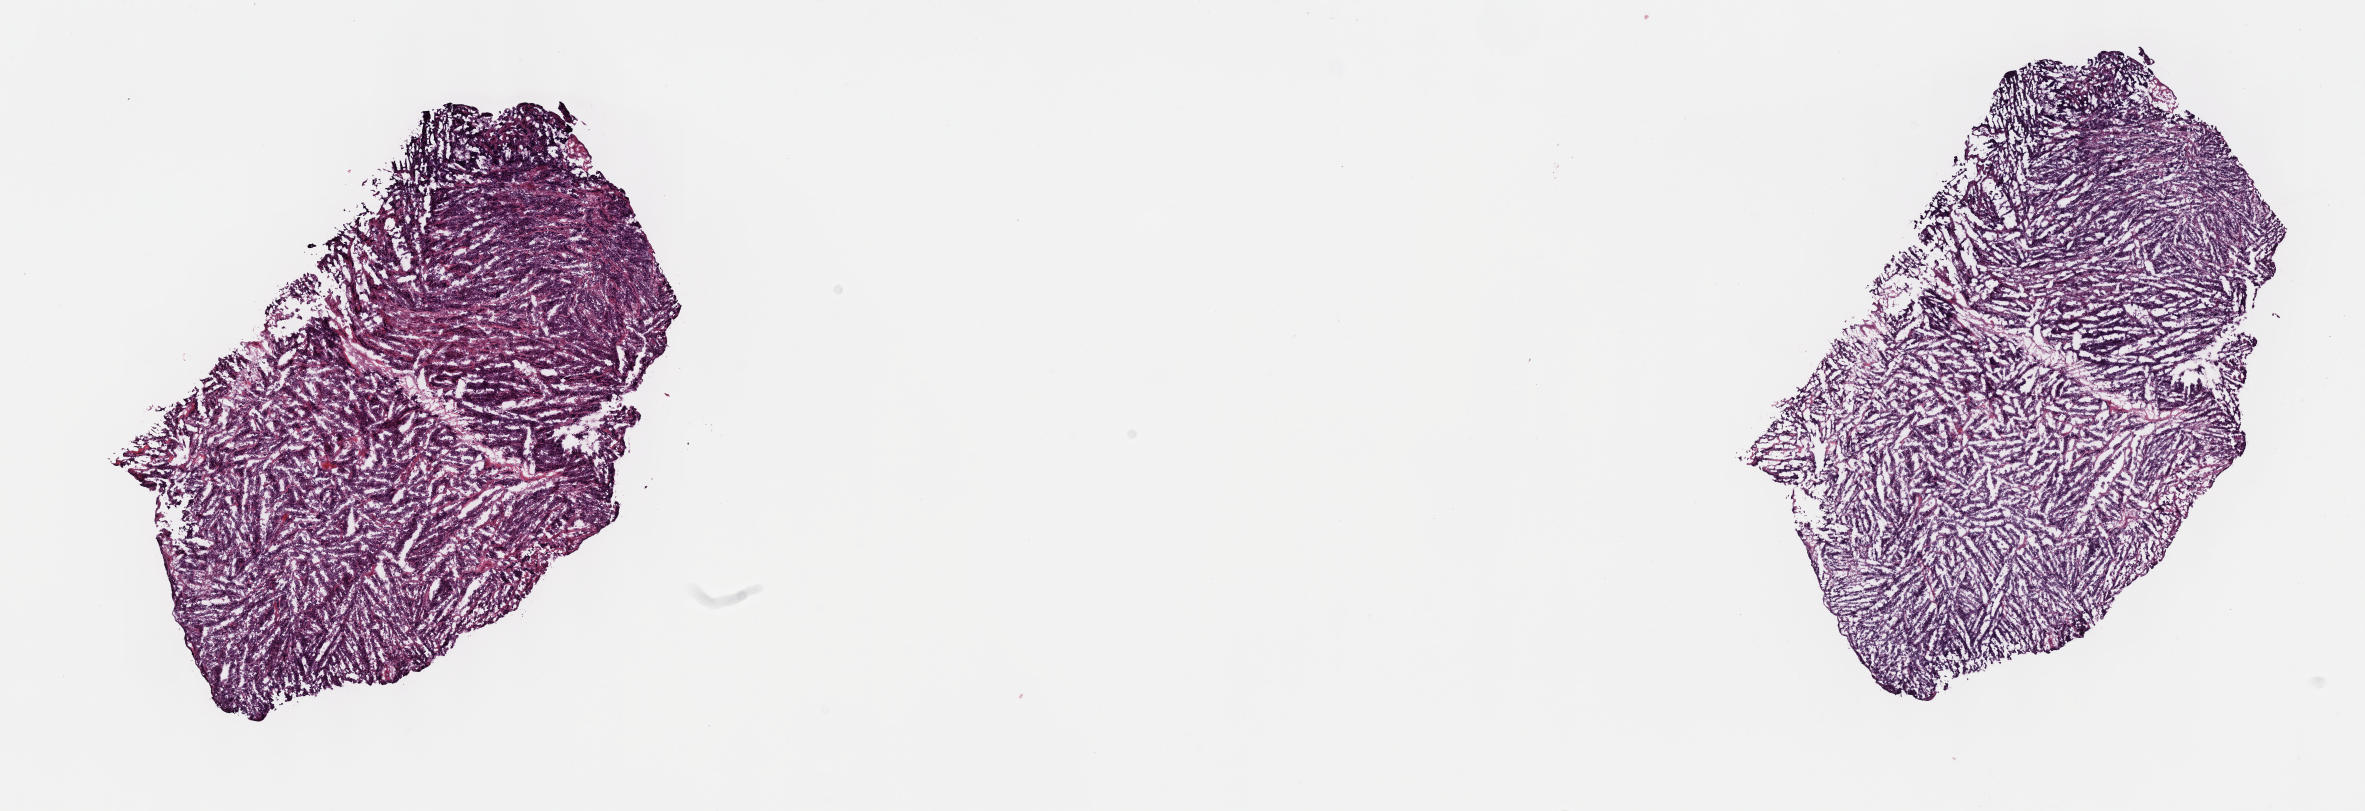
Whole-slide histology image, H&E, a low-resolution overview of the entire scanned area, about 19.1 x 6.6 mm, frozen section, primary tumour sample from the thymus. Female, age 71 years at initial diagnosis. Pathologist review of this section (percent, as recorded): tumour cells 80%, tumour nuclei 80%.
Pathologic diagnosis: Thymic carcinoma, NOS (anterior mediastinum).